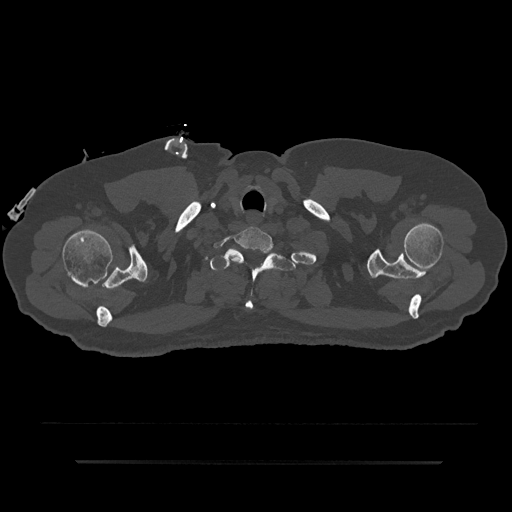
CT including the spine, one axial slice. Slice 752 of 797 in the series (ordered by position). Bone window (W 1800 / L 400 HU). 0.5 mm slice thickness. 512 × 512 image matrix. Male patient, age 59 years. From the clinical record (not read from this slice): primary cancer: bile ducts; vertebrae with lytic lesions (as recorded): T10.
Outlined on this slice (semi-automatic segmentation, software-assisted and operator-edited):
- T1 vertebra: bounding box [x1, y1, x2, y2] px = [210, 249, 295, 310]